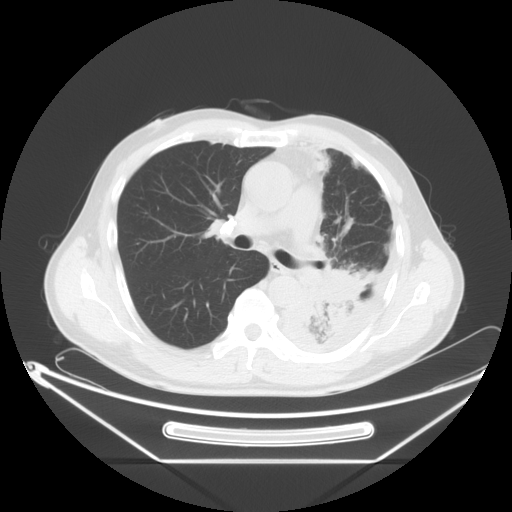
Chest CT, one axial slice. Slice 38 of 63 in the series (ordered by position). Reconstruction kernel STANDARD. 120 kVp. Lung window (W 1500 / L -600 HU). 5 mm slice thickness. 512 × 512 image matrix, field of view 442 × 442 mm. Male patient, age 60 years. From the clinical record (not read from this slice): clinical TNM (as recorded): T4 N1 M1.
Annotated regions visible in this slice (bounding box drawn by a radiologist):
- lung tumour (recorded histology: adenocarcinoma): bounding box <295,251,369,336> (left, top, right, bottom; pixels)